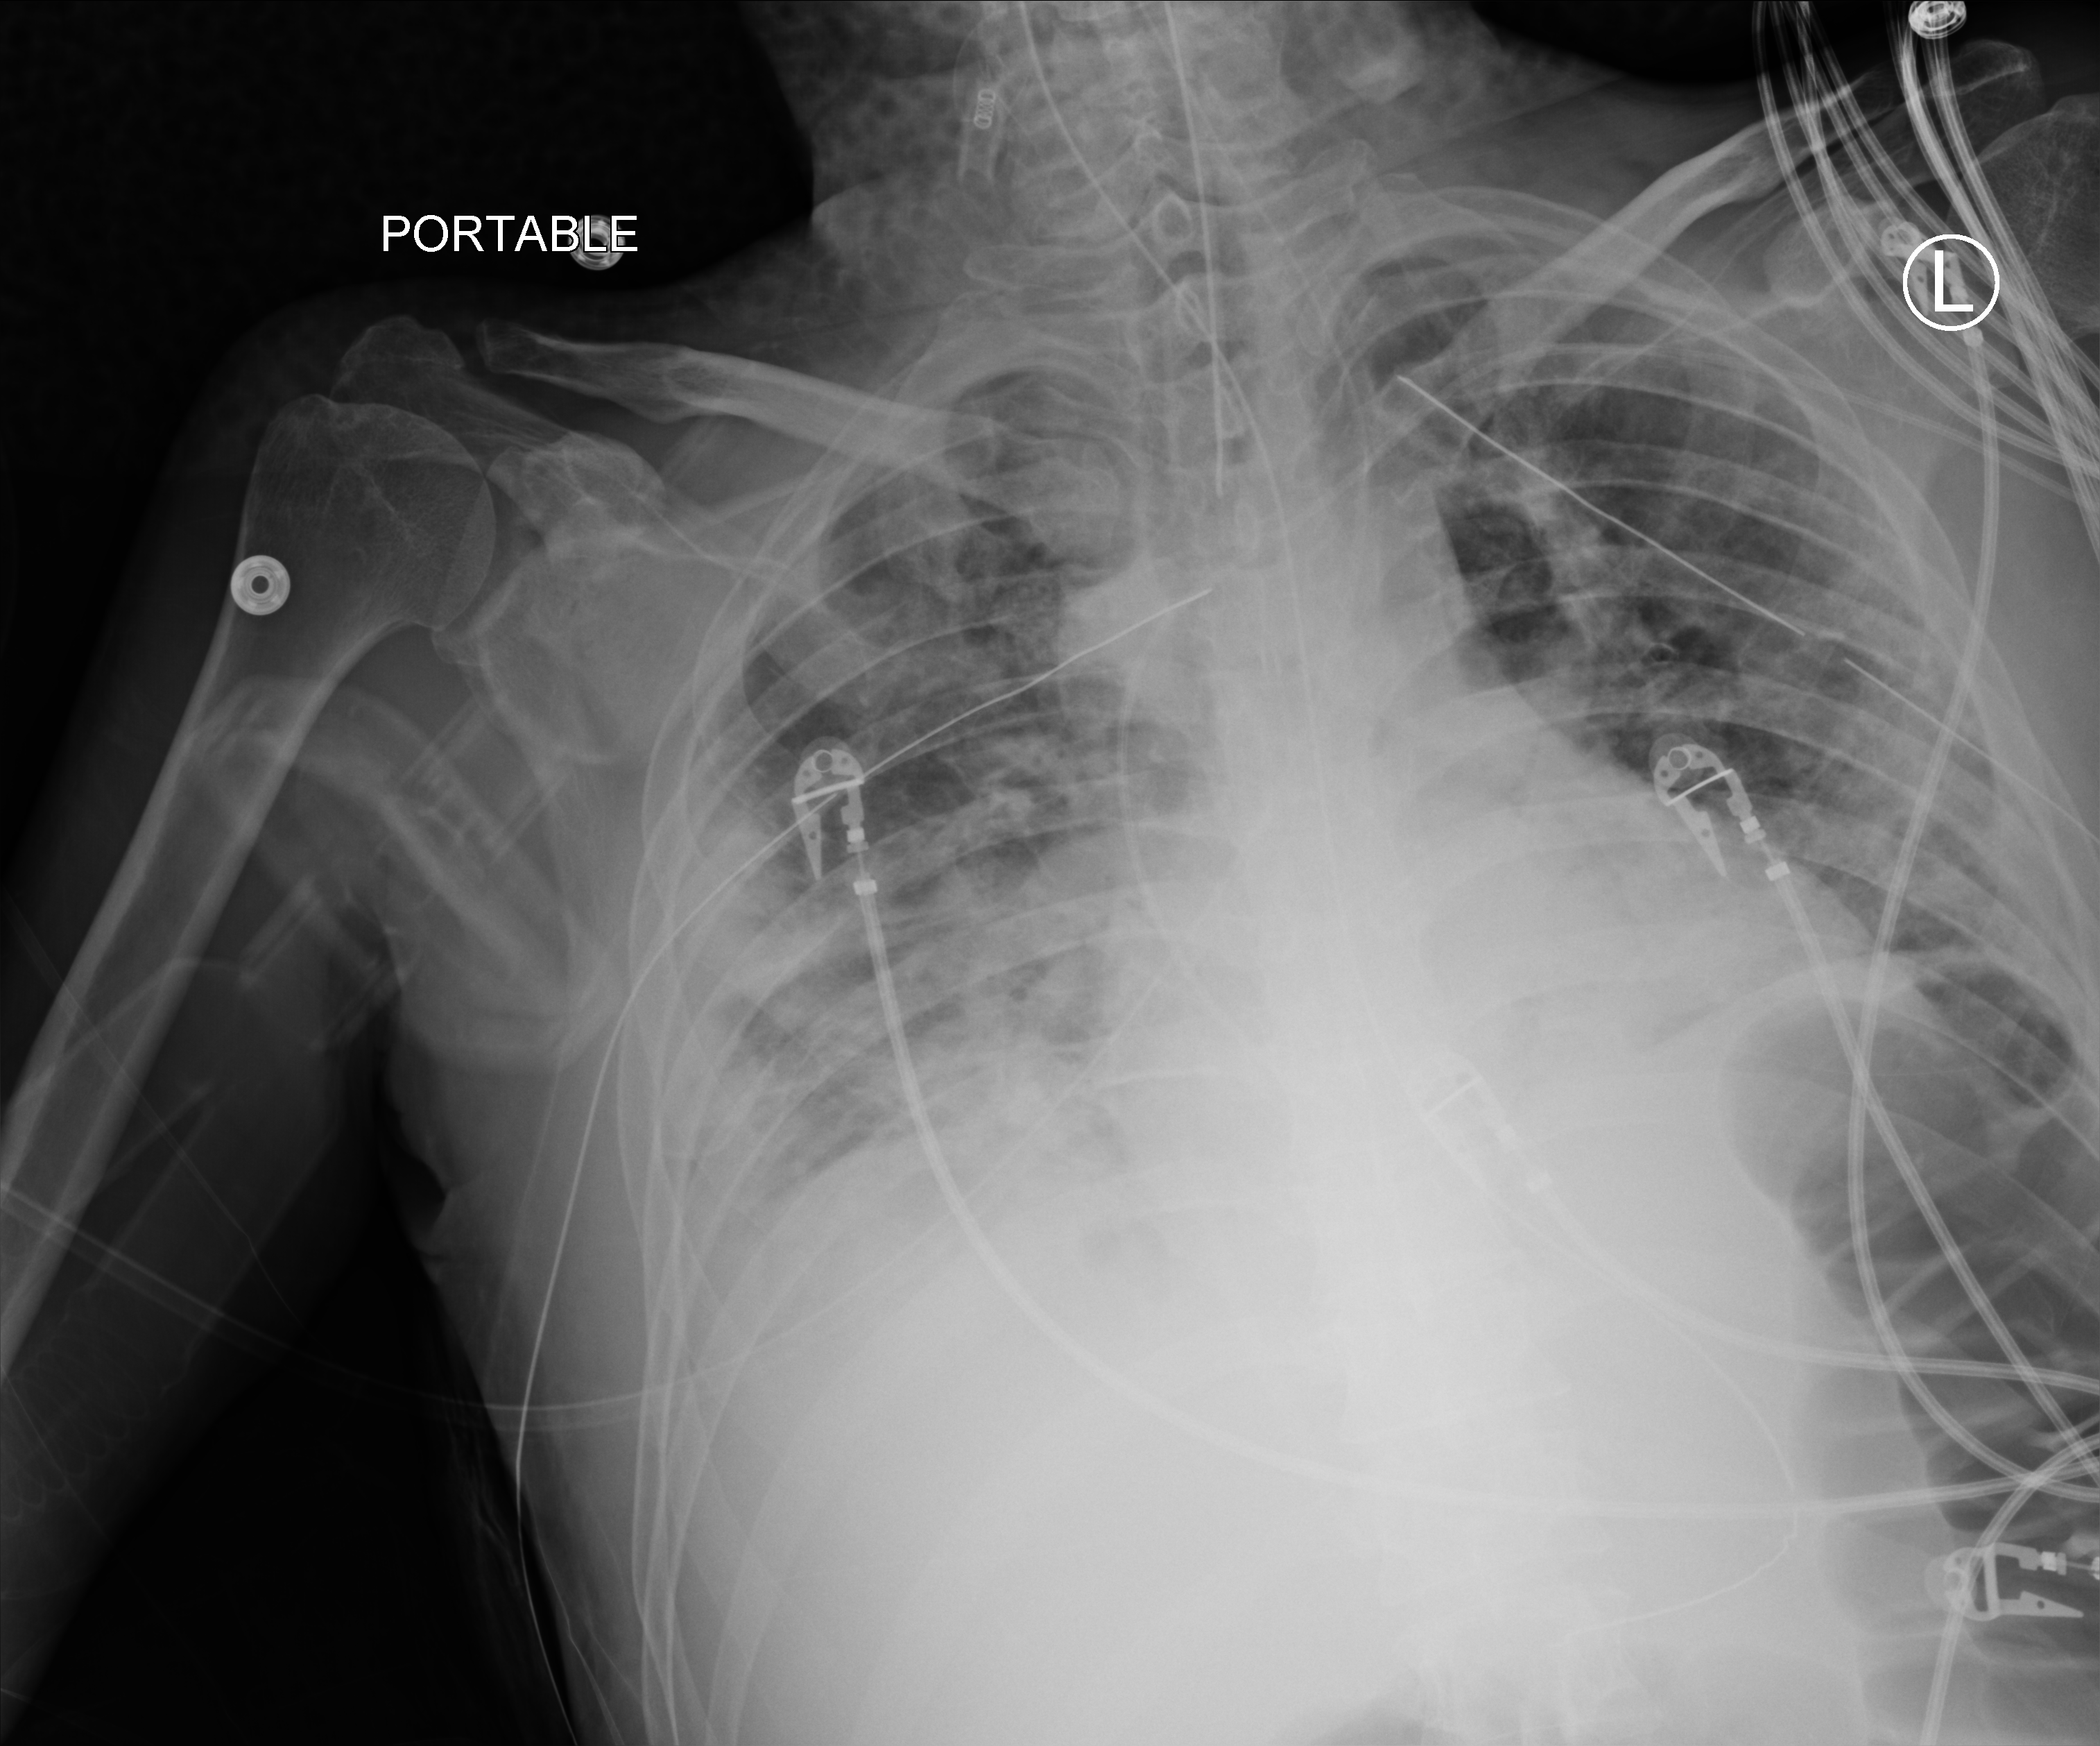
Portable chest radiograph; anteroposterior (AP) projection. Patient hospitalised with COVID-19; male, aged 18–59 years.
Hospital-stay facts (about this admission, not read from this image; timing relative to this image not recorded): other chronic lung disease (admission record): no; chronic kidney disease (admission record): no.